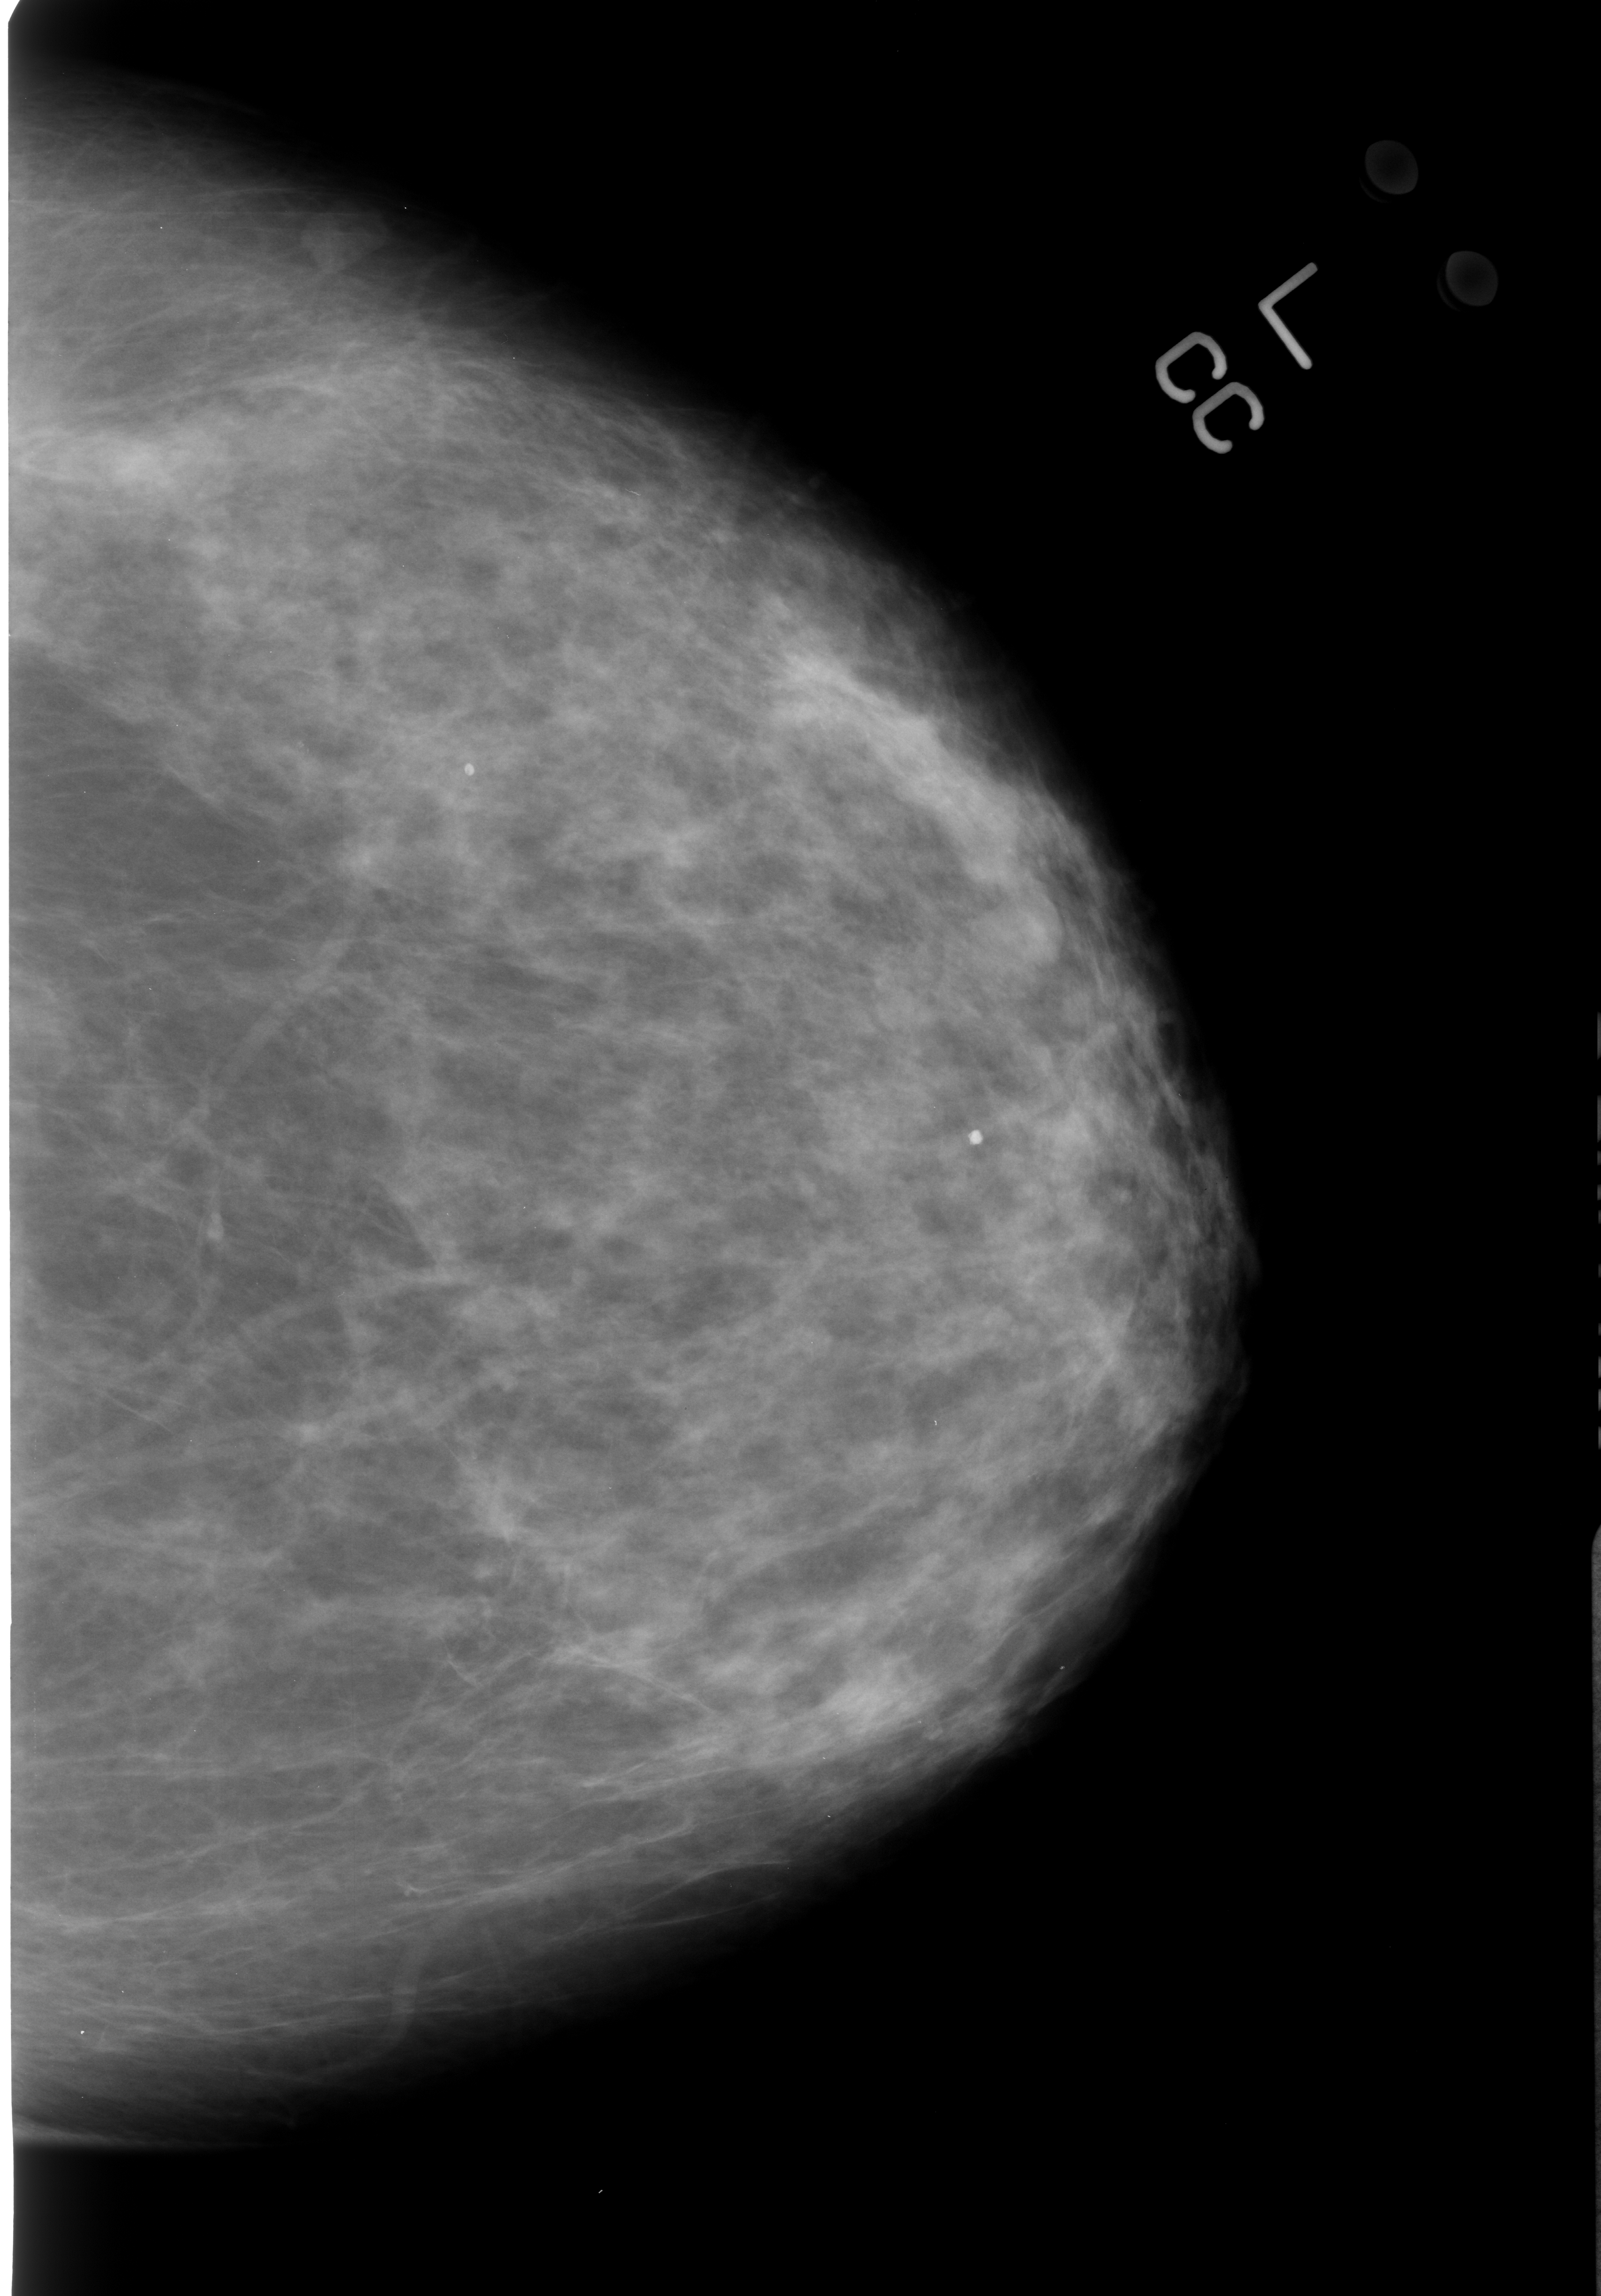
Mammogram (digitized film); left breast; CC view; BI-RADS breast density category 2 (scale 1–4).
- Marked findings (only marked abnormalities are described; nothing is implied about the rest of the image): Finding 1 of 2: calcifications, morphology coarse / round and regular / lucent center; BI-RADS assessment category 2; benign; no additional work-up was recommended (benign without callback).
- Finding 2 of 2: calcifications, morphology coarse / round and regular / lucent center; BI-RADS assessment category 2; subtlety rating 4 on a 1 (subtle) to 5 (obvious) scale; benign without callback (not worked up further).